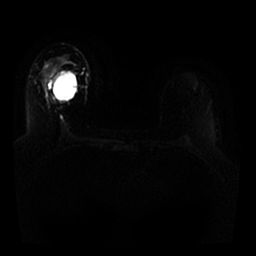
Breast MRI, one axial slice. Slice 17 of 25 in the series (ordered by position). Diffusion-weighted series; image 2 of 4 stored at this slice position (different b-values; order by instance number). 1.5 T. 4 mm slice thickness. 256 × 256 image matrix, field of view 330 × 330 mm. Female patient.
Outlined on this slice (outlined manually by an expert reader):
- tumour on diffusion-weighted imaging: bounding box <52,72,61,81> (left, top, right, bottom; pixels)